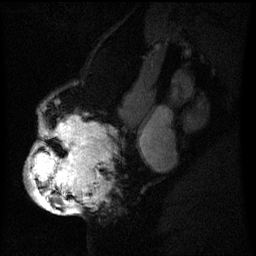
Breast MRI (dynamic contrast-enhanced), one sagittal slice. Dynamic contrast-enhanced series, image 2 of 3 at this slice position (ordered by acquisition). 1.5 T. TE 4.2 ms, TR 8 ms. 2.2 mm slice thickness. 256 × 256 image matrix, field of view 200 × 200 mm. Patient: female, 50 years.
Annotated regions visible in this slice (semi-automatic segmentation, software-assisted and operator-edited):
- analysis volume of interest (the breast-tissue region the enhancement analysis was run in; not a lesion): bounding box <28,116,109,211> (left, top, right, bottom; pixels)
- tumour enhancement mask (voxels above the 70 % enhancement threshold inside the analysis volume of interest): <29,120,100,211>